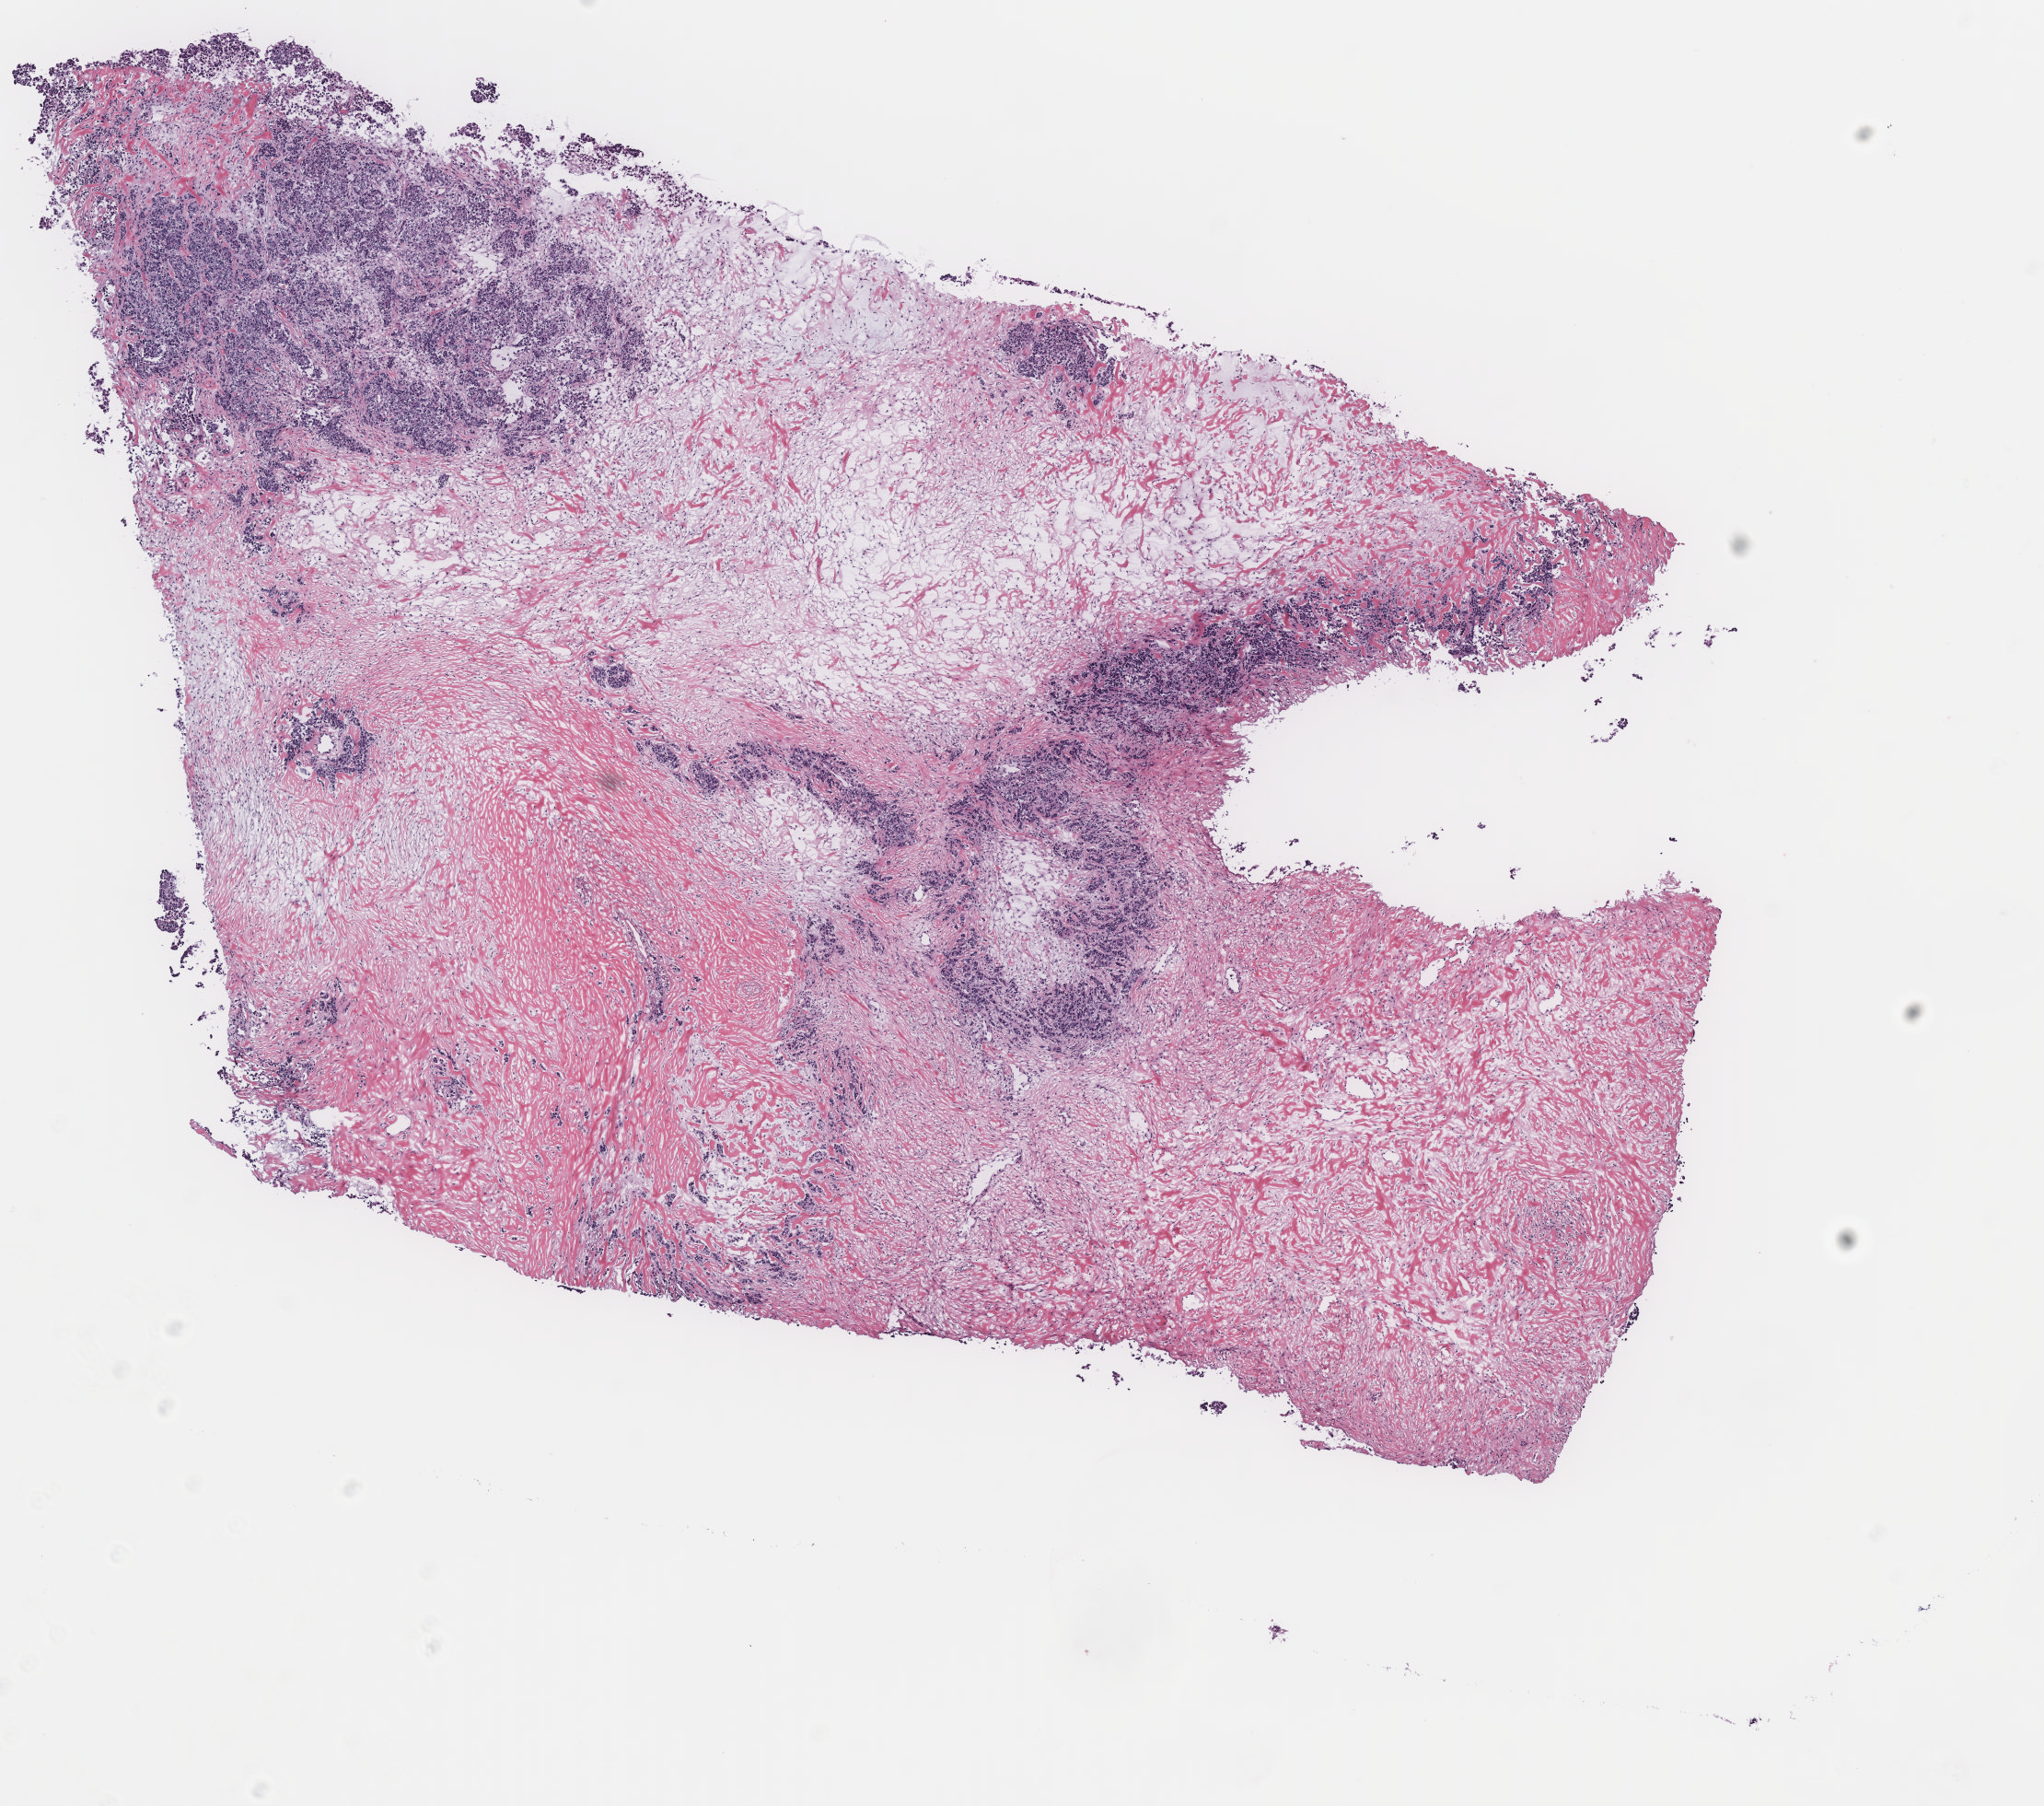
Digitized Hematoxylin and eosin (H&E) stained tissue section (whole slide) — a low-resolution overview of the entire scanned area, about 8.9 x 7.8 mm. Tumour tissue sample, breast. Female, 75 y/o.
- histologic diagnosis: Infiltrating duct carcinoma, NOS
- AJCC pathologic stage: IIIB